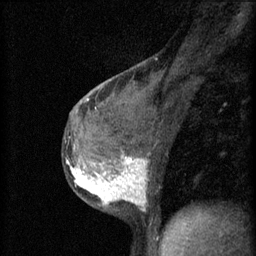
Breast MRI (dynamic contrast-enhanced), one sagittal slice; position 32 of 60 along the scan axis; 3 images stored at this slice position (order not interpretable as contrast timing); 1.5 T; TE 4.2 ms, TR 11 ms; 256 × 256 image matrix. Female patient, age 37 years.
Structures marked on this image (semi-automatically segmented with operator editing):
- analysis volume of interest (the breast-tissue region the enhancement analysis was run in; not a lesion): bounding box (x1, y1, x2, y2) in pixels: (65, 138, 152, 213)
- tumour enhancement mask (voxels above the 70 % enhancement threshold inside the analysis volume of interest): (66, 156, 147, 207)